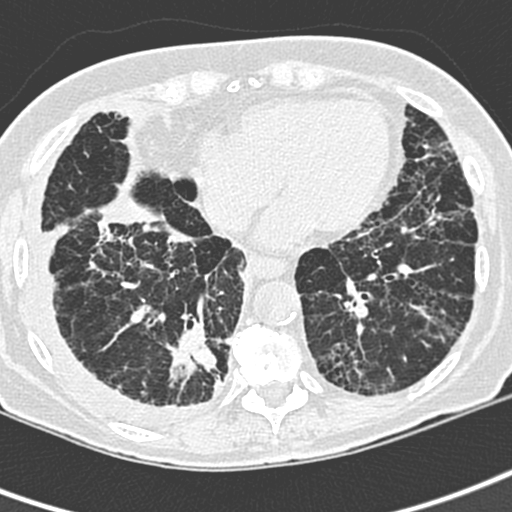
Low-dose screening chest CT, one axial slice. Slice 88 of 220 in the series (ordered by position). 120 kVp. Lung window (W 1500 / L -600 HU). 1.3 mm slice thickness. 512 × 512 image matrix, field of view 288 × 288 mm.
Structures marked on this image (outlined manually by an expert reader):
- lesion 1 (tumor, lower lobe of right lung): bounding box (x1, y1, x2, y2) in pixels: (169, 346, 217, 379)